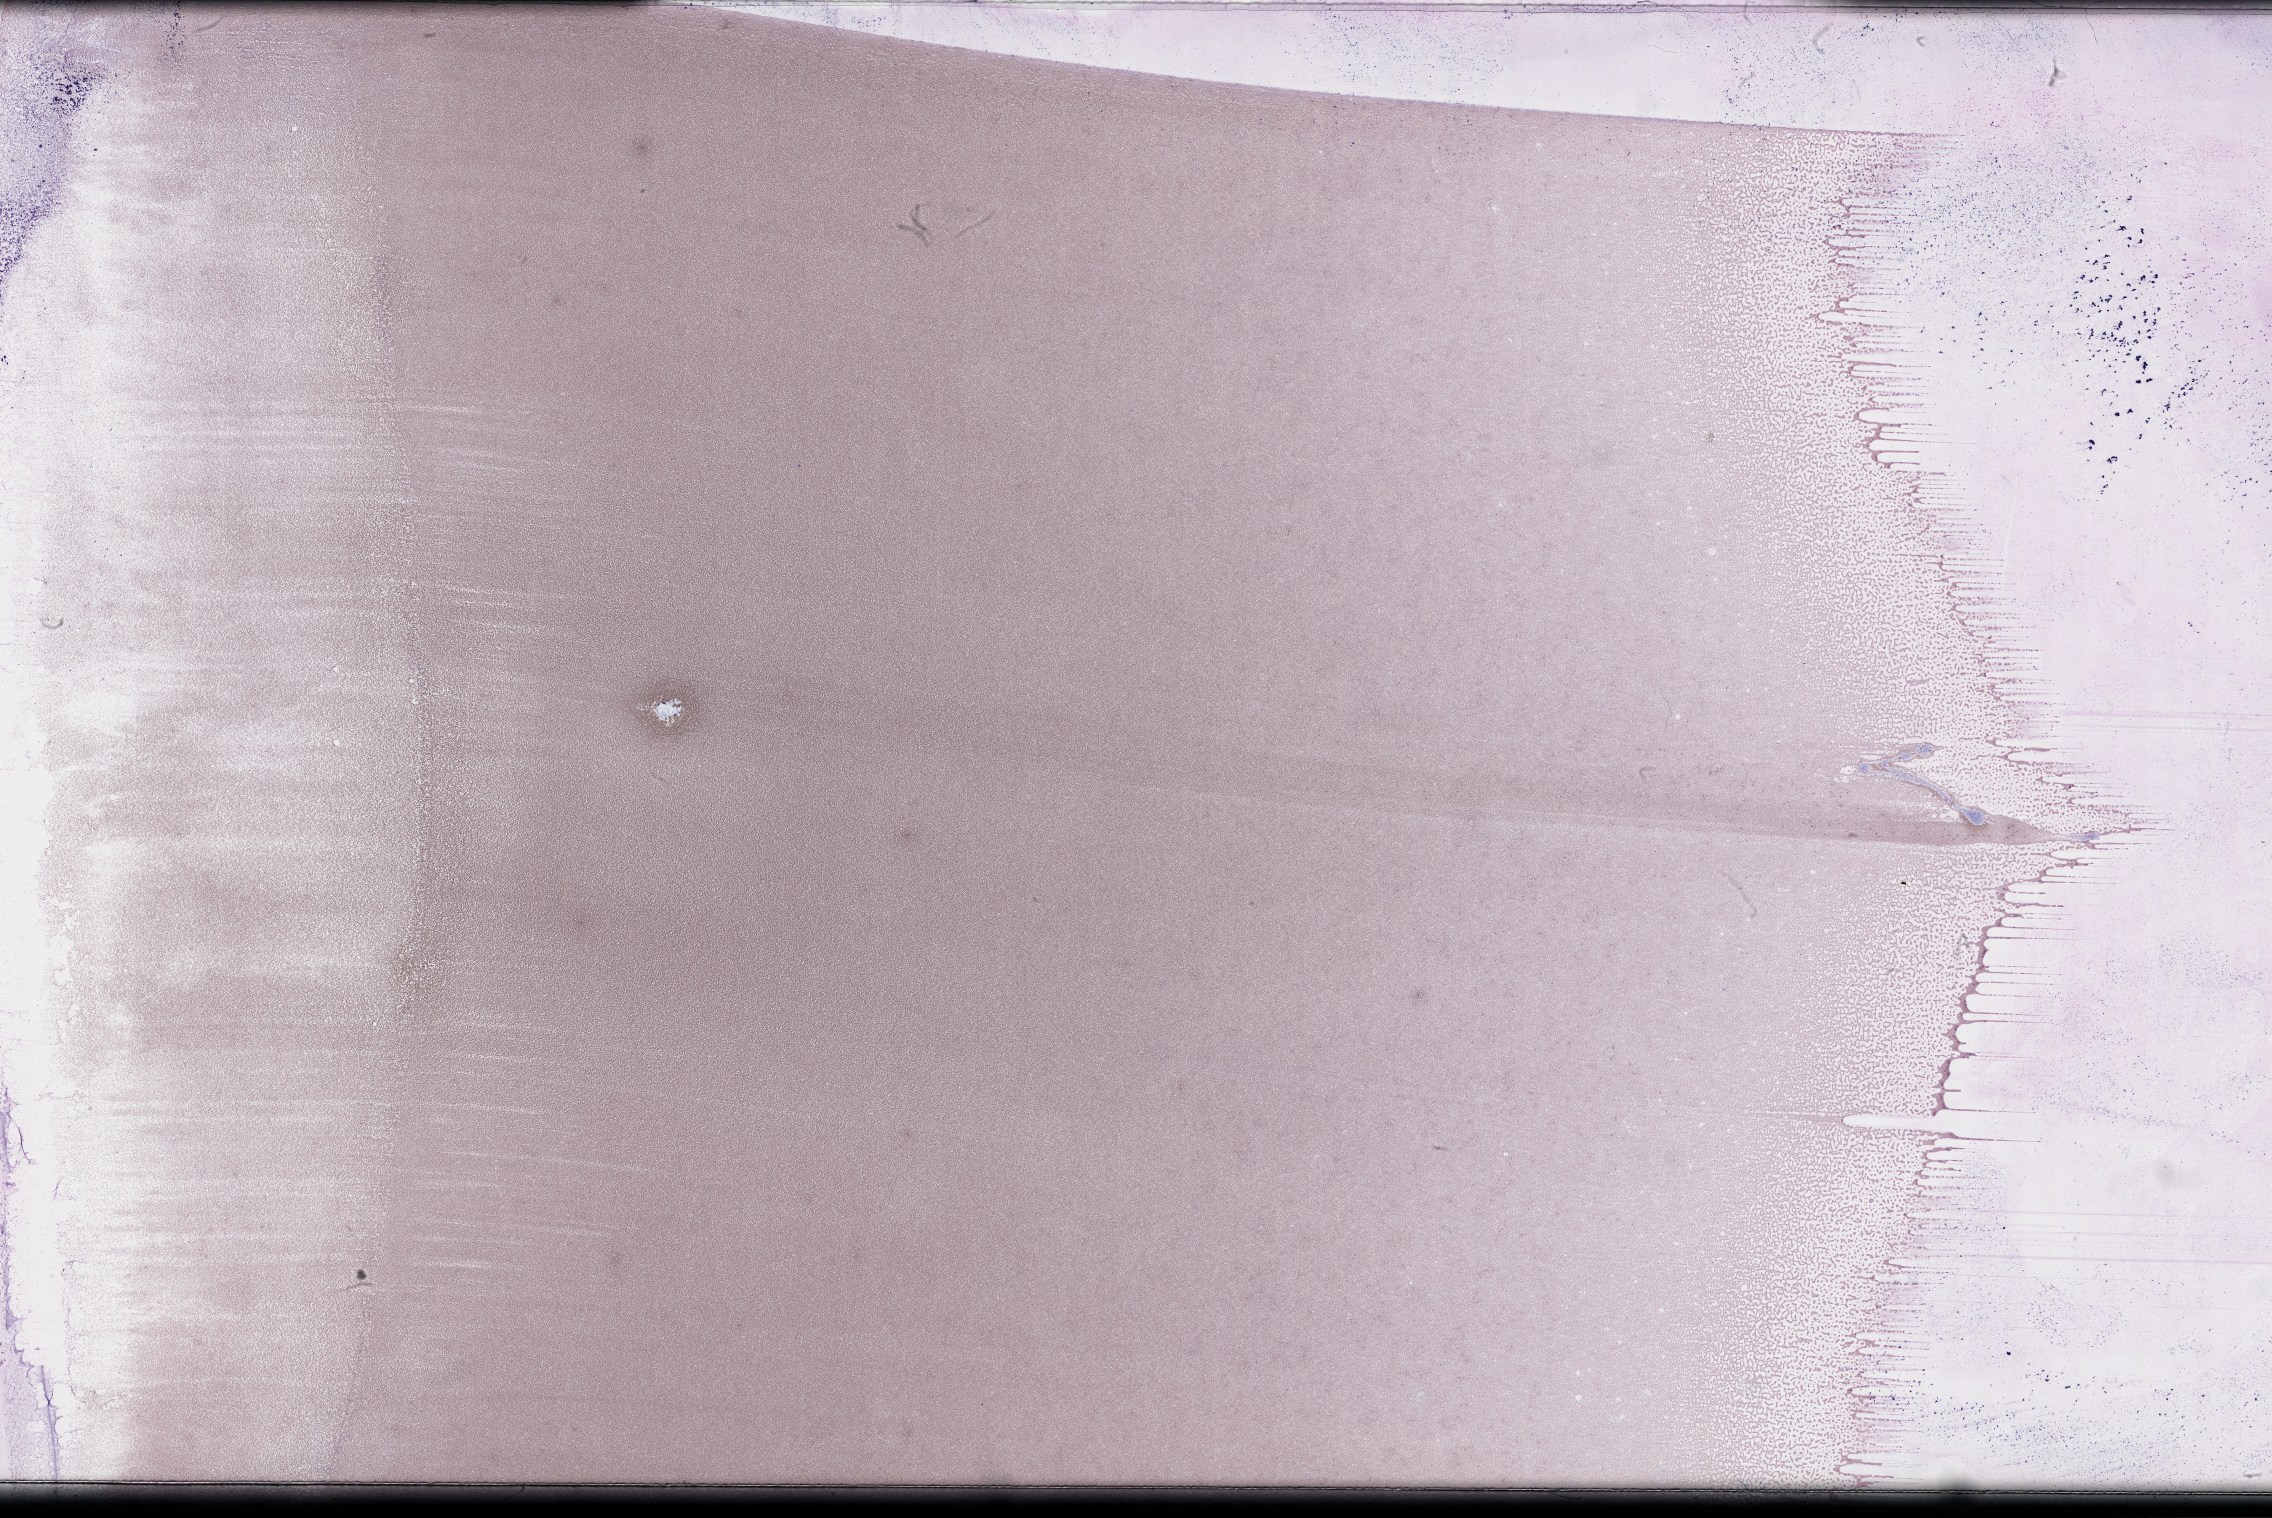
Wright-Giemsa-stained whole blood smear, whole-slide image, whole scanned area (about 36.7 x 24.5 mm) shown as a low-resolution overview. Smear from an EDTA sample. Specimen time point: collected at baseline (before treatment). Male patient.
Patient diagnosis: Plasma Cell Myeloma.